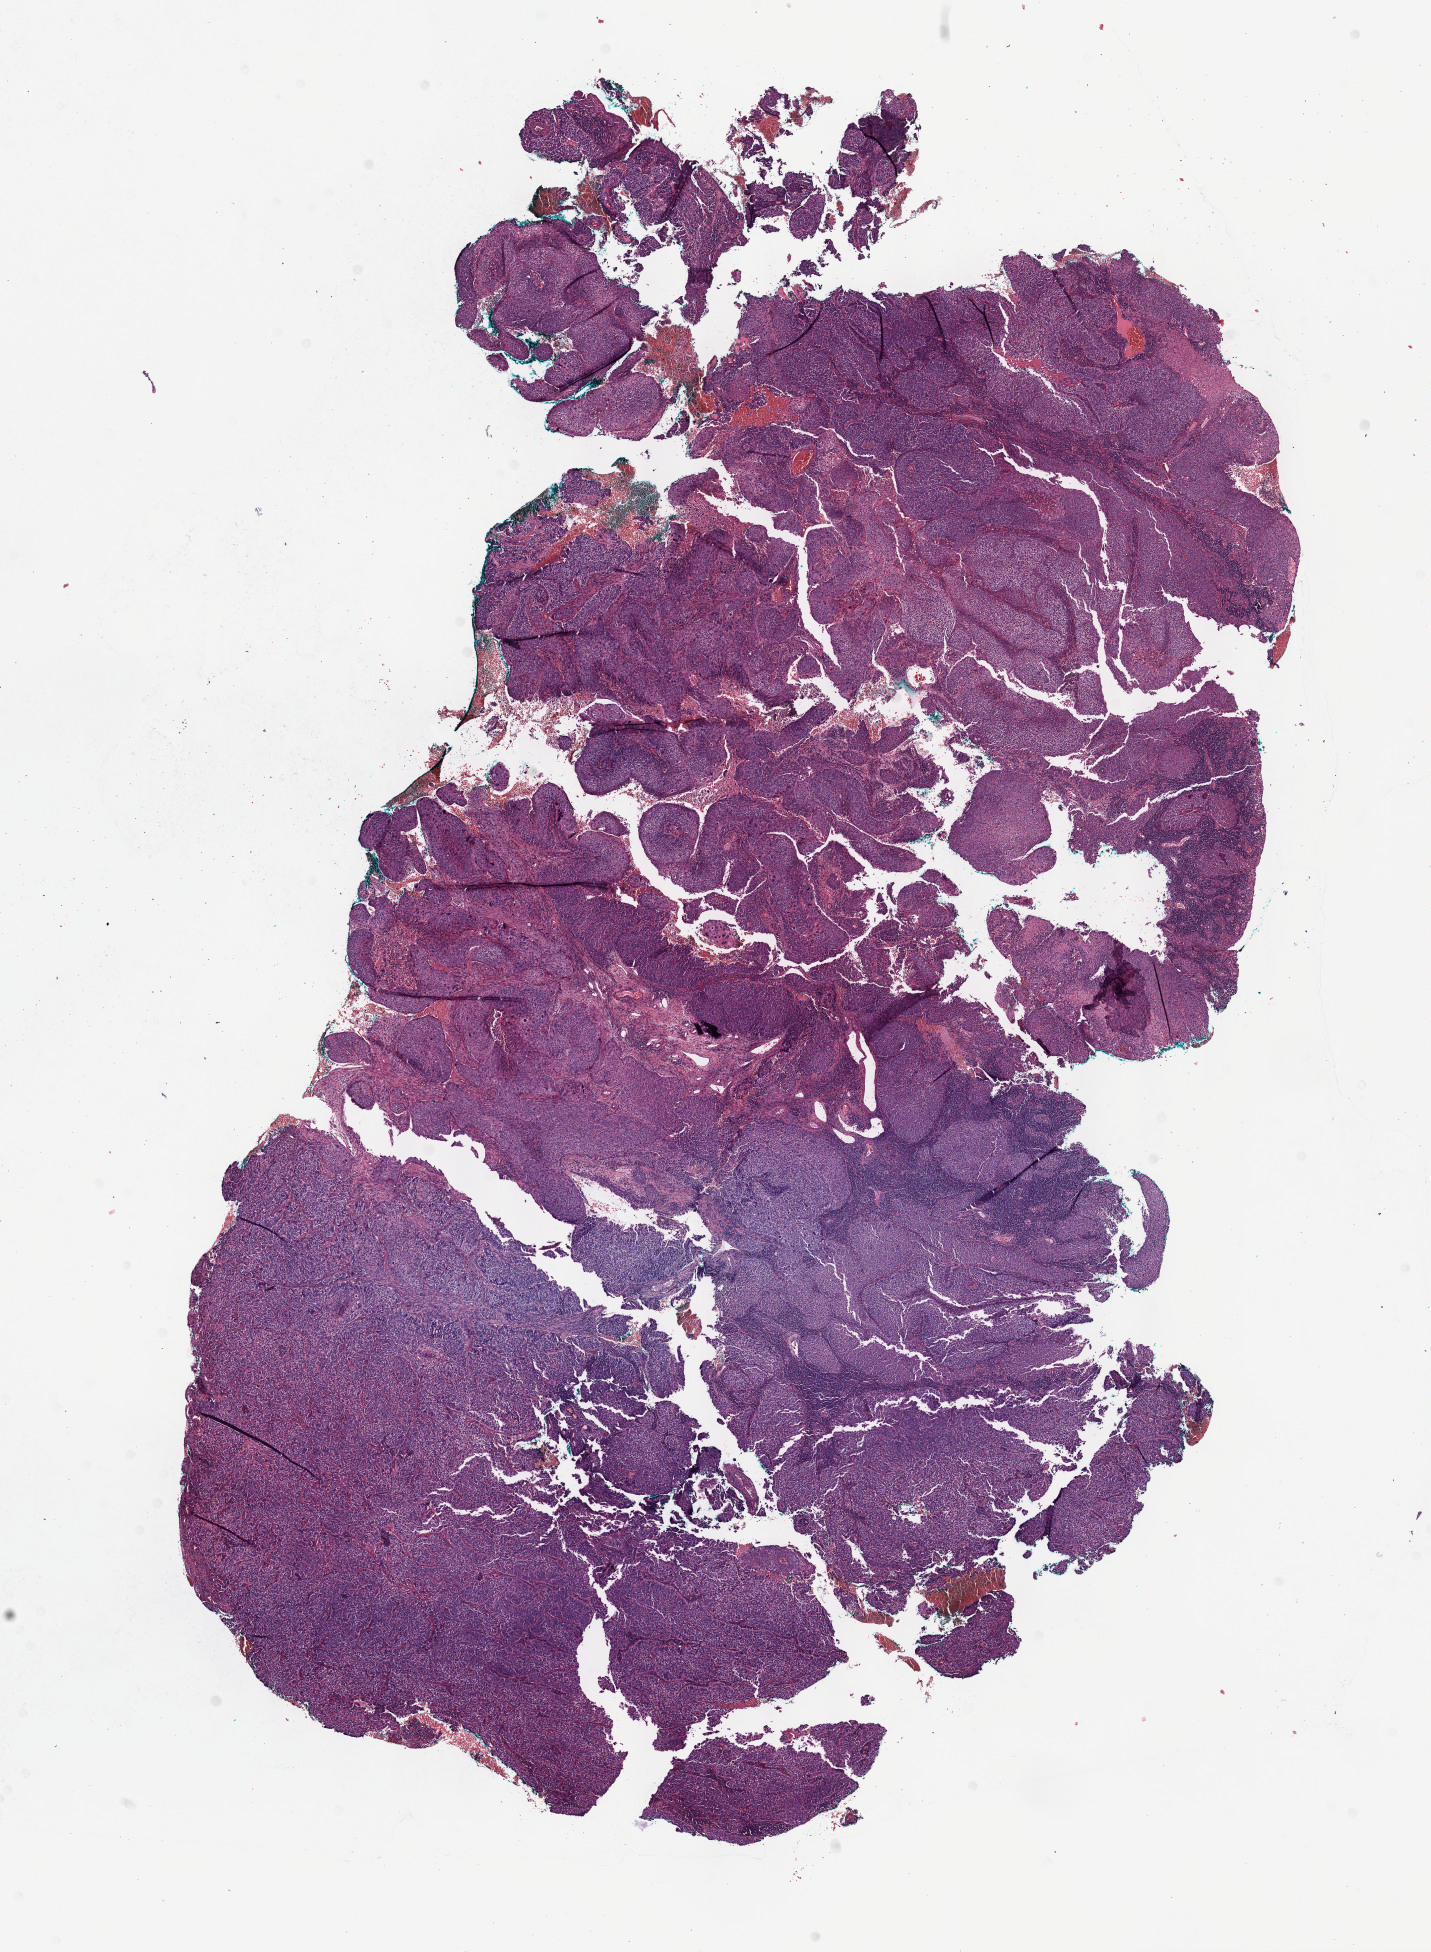
Digitized H&E tissue section (whole slide), whole scanned area (about 11.6 x 15.8 mm, acquisition: 40x scan) shown as a low-resolution overview, formalin-fixed paraffin-embedded (FFPE) diagnostic section, cervix, primary tumour sample. Female, age 52 years at initial diagnosis.
Histologic diagnosis: Squamous cell carcinoma, large cell, nonkeratinizing, NOS (cervix uteri).